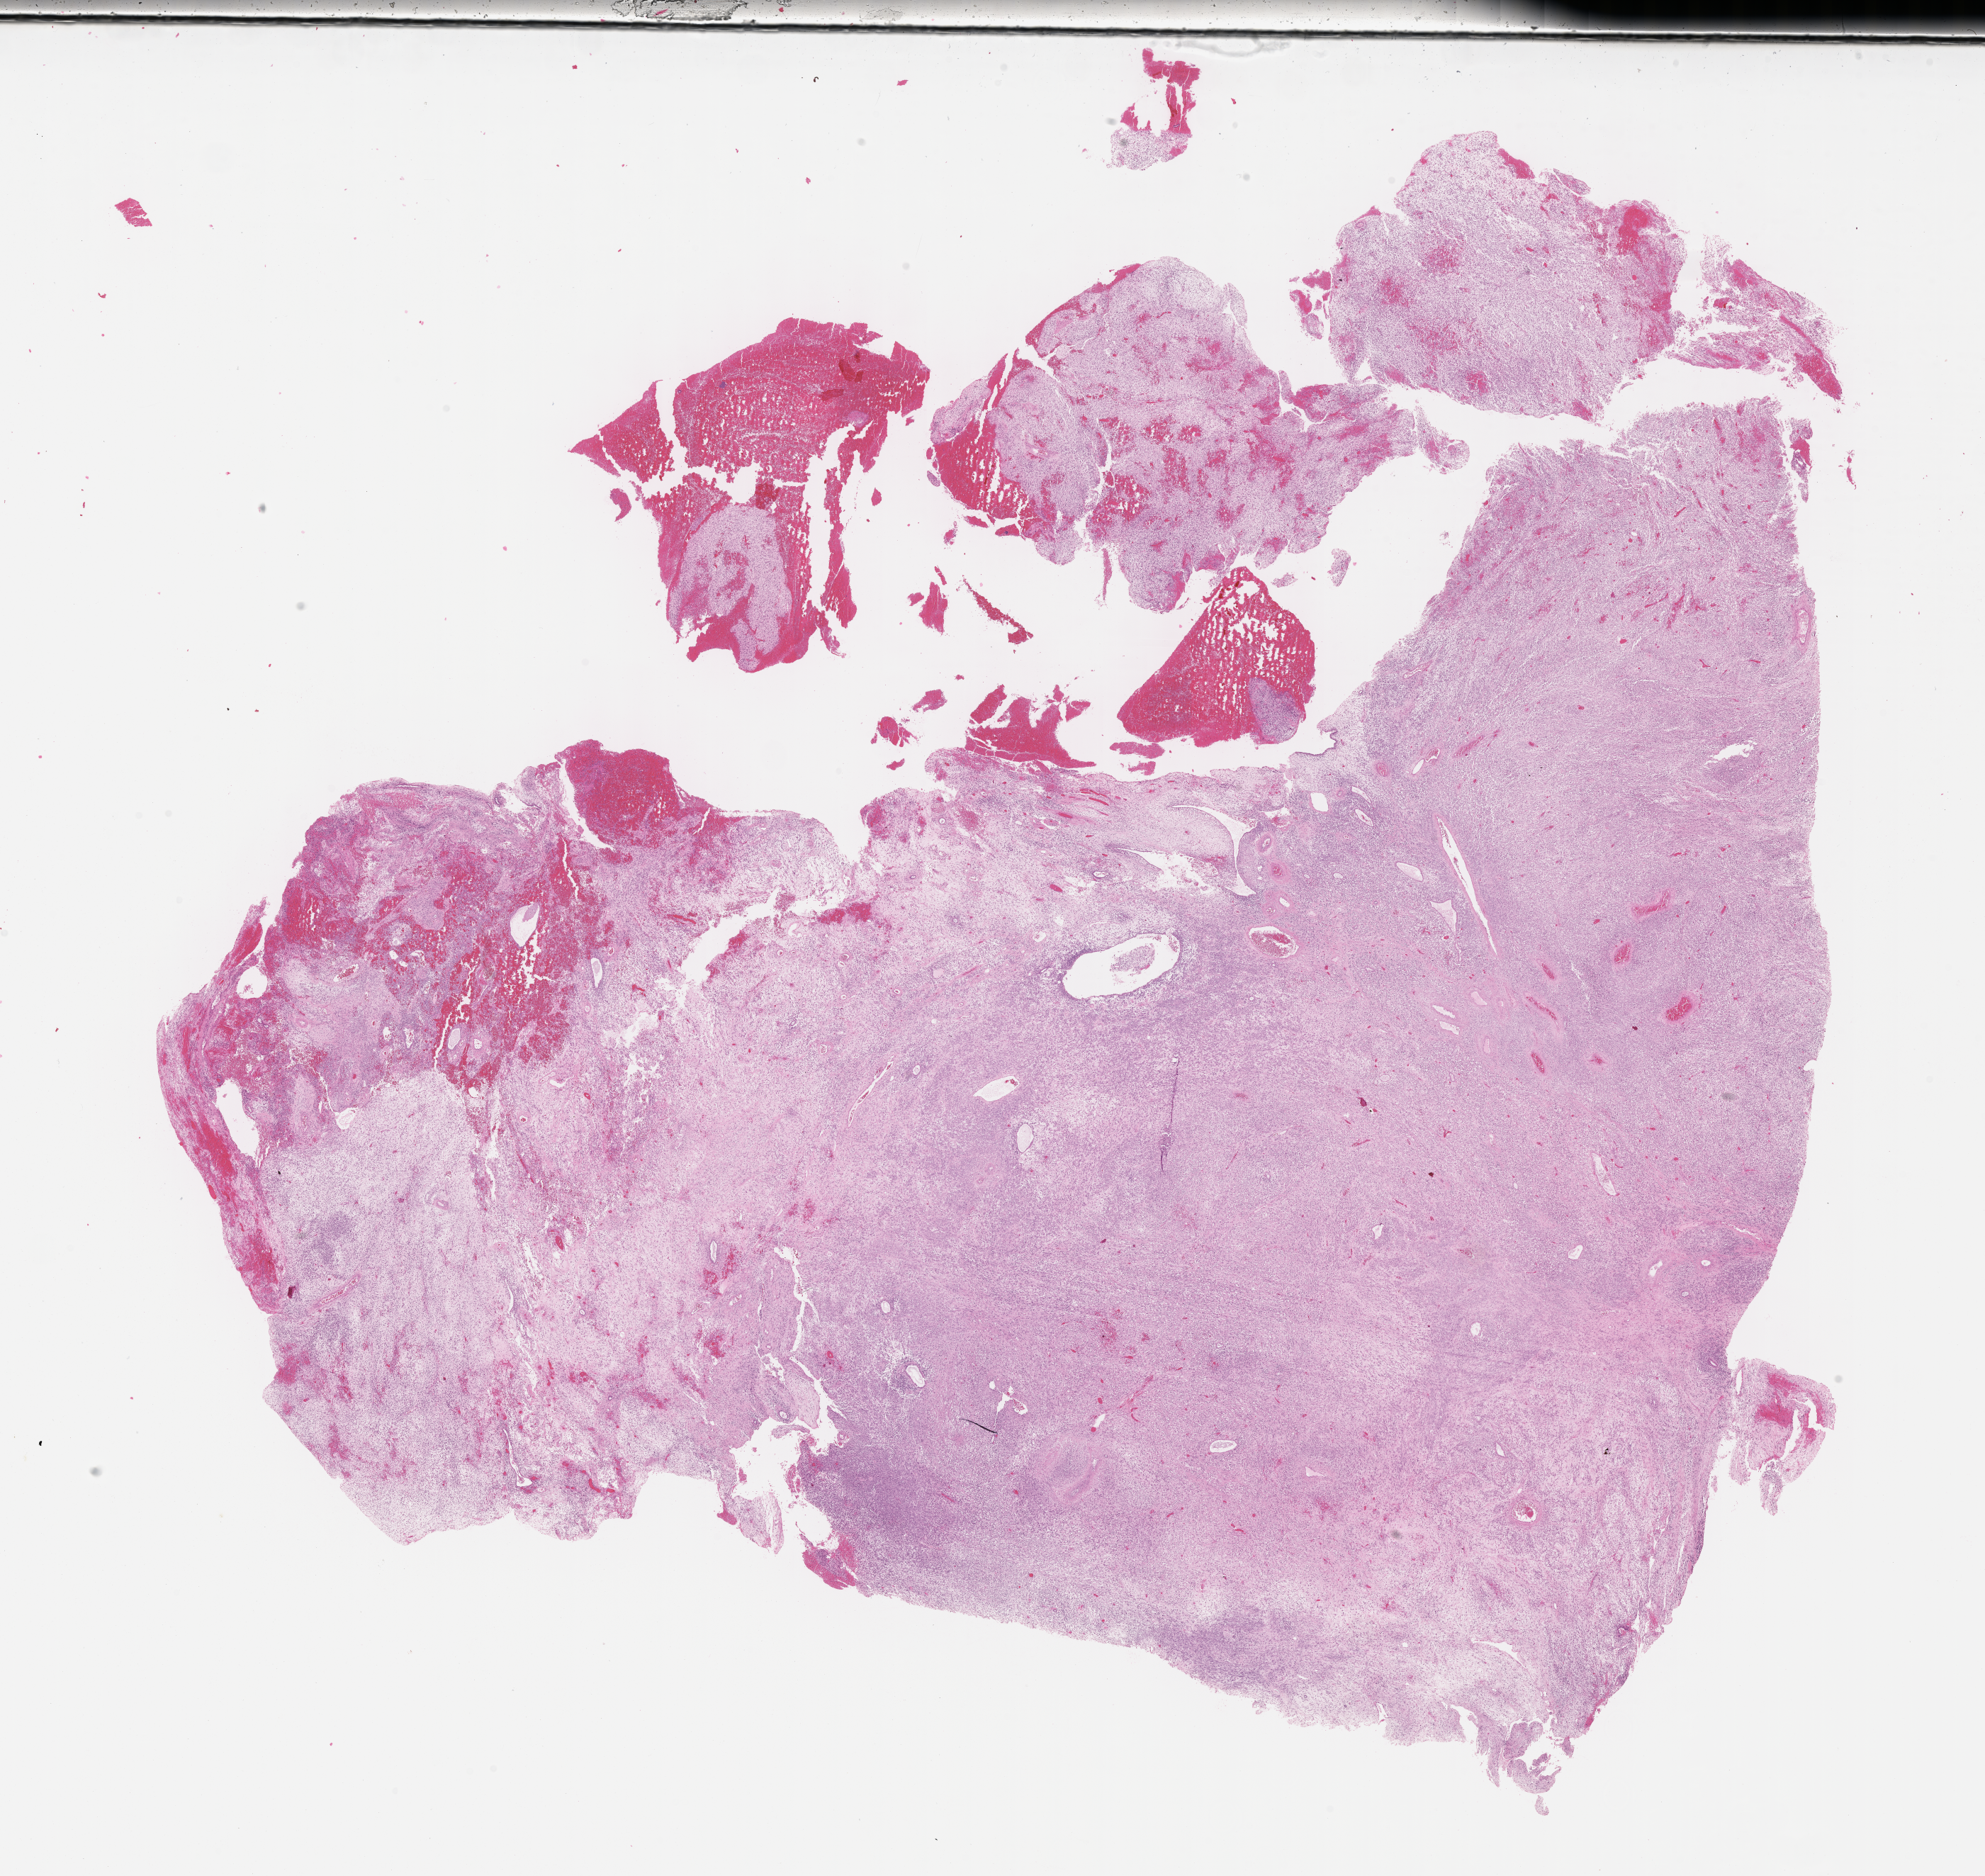
Whole-slide image, hematoxylin and eosin (H&E) stain of tumor tissue — whole scanned area (about 22.6 x 21.4 mm) shown as a low-resolution overview; formalin-fixed, paraffin-embedded (FFPE) tissue; site: uterus. Female patient, age at diagnosis 17.6 years.
Diagnosis: rhabdomyosarcoma; histological classification: embryonal rhabdomyosarcoma.